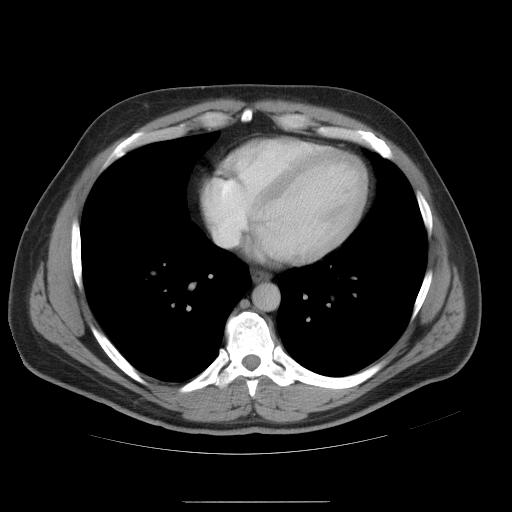
Contrast-enhanced abdominal CT, one axial slice. Slice 53 of 54 in the series (ordered by position). Soft-tissue window (W 400 / L 40 HU). 5 mm slice thickness. 512 × 512 image matrix. Male patient, age 40 years. From the clinical record (not read from this slice): diagnosis: colorectal cancer liver metastases, imaged before liver resection; multiple liver metastases: no; largest metastasis: 15 cm; disease in both lobes: no.
Annotated regions visible in this slice (expert manual segmentation):
- hepatic veins: bounding box (x1, y1, x2, y2) in pixels: (207, 201, 261, 246)